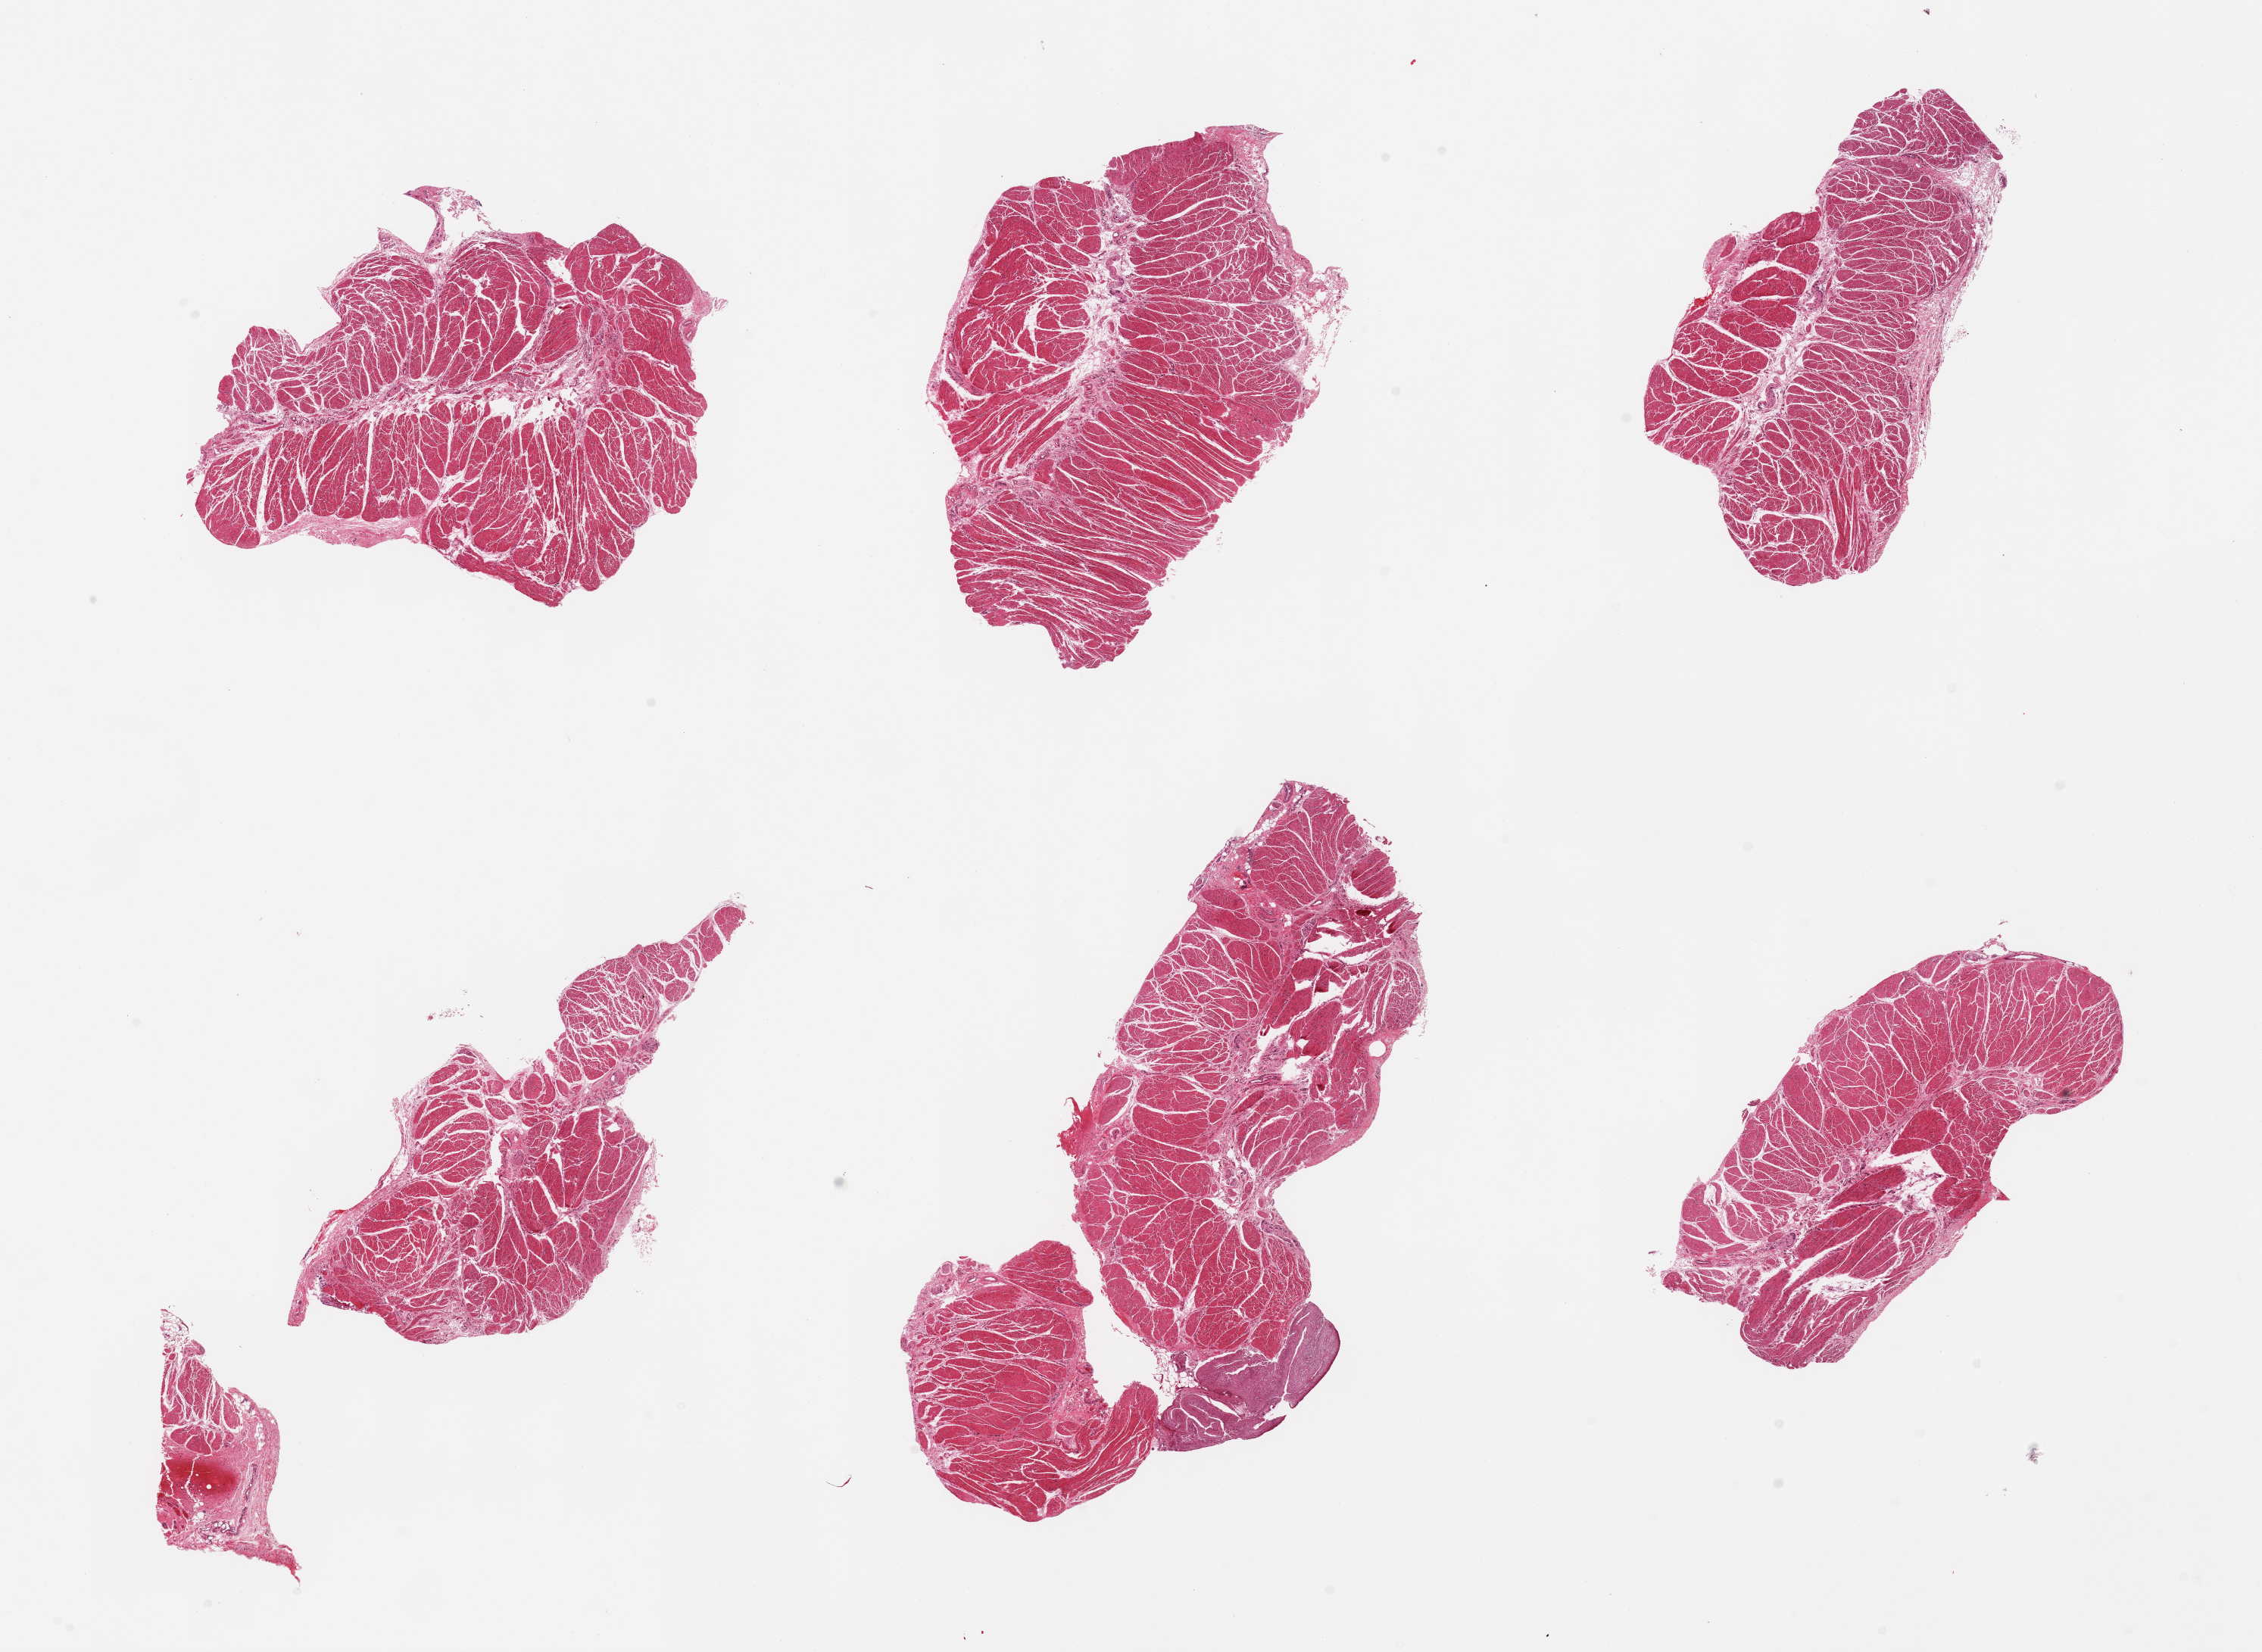
Digitized H&E-stained section — whole scanned area (about 23.6 x 17.3 mm, from a 20x scan) shown as a low-resolution overview, PAXgene-fixed paraffin-embedded (PFPE) section, target tissue: esophageal muscle, donor tissue sample. Donor: female.
* review note (as recorded): 6 pieces, confirmed target muscularis